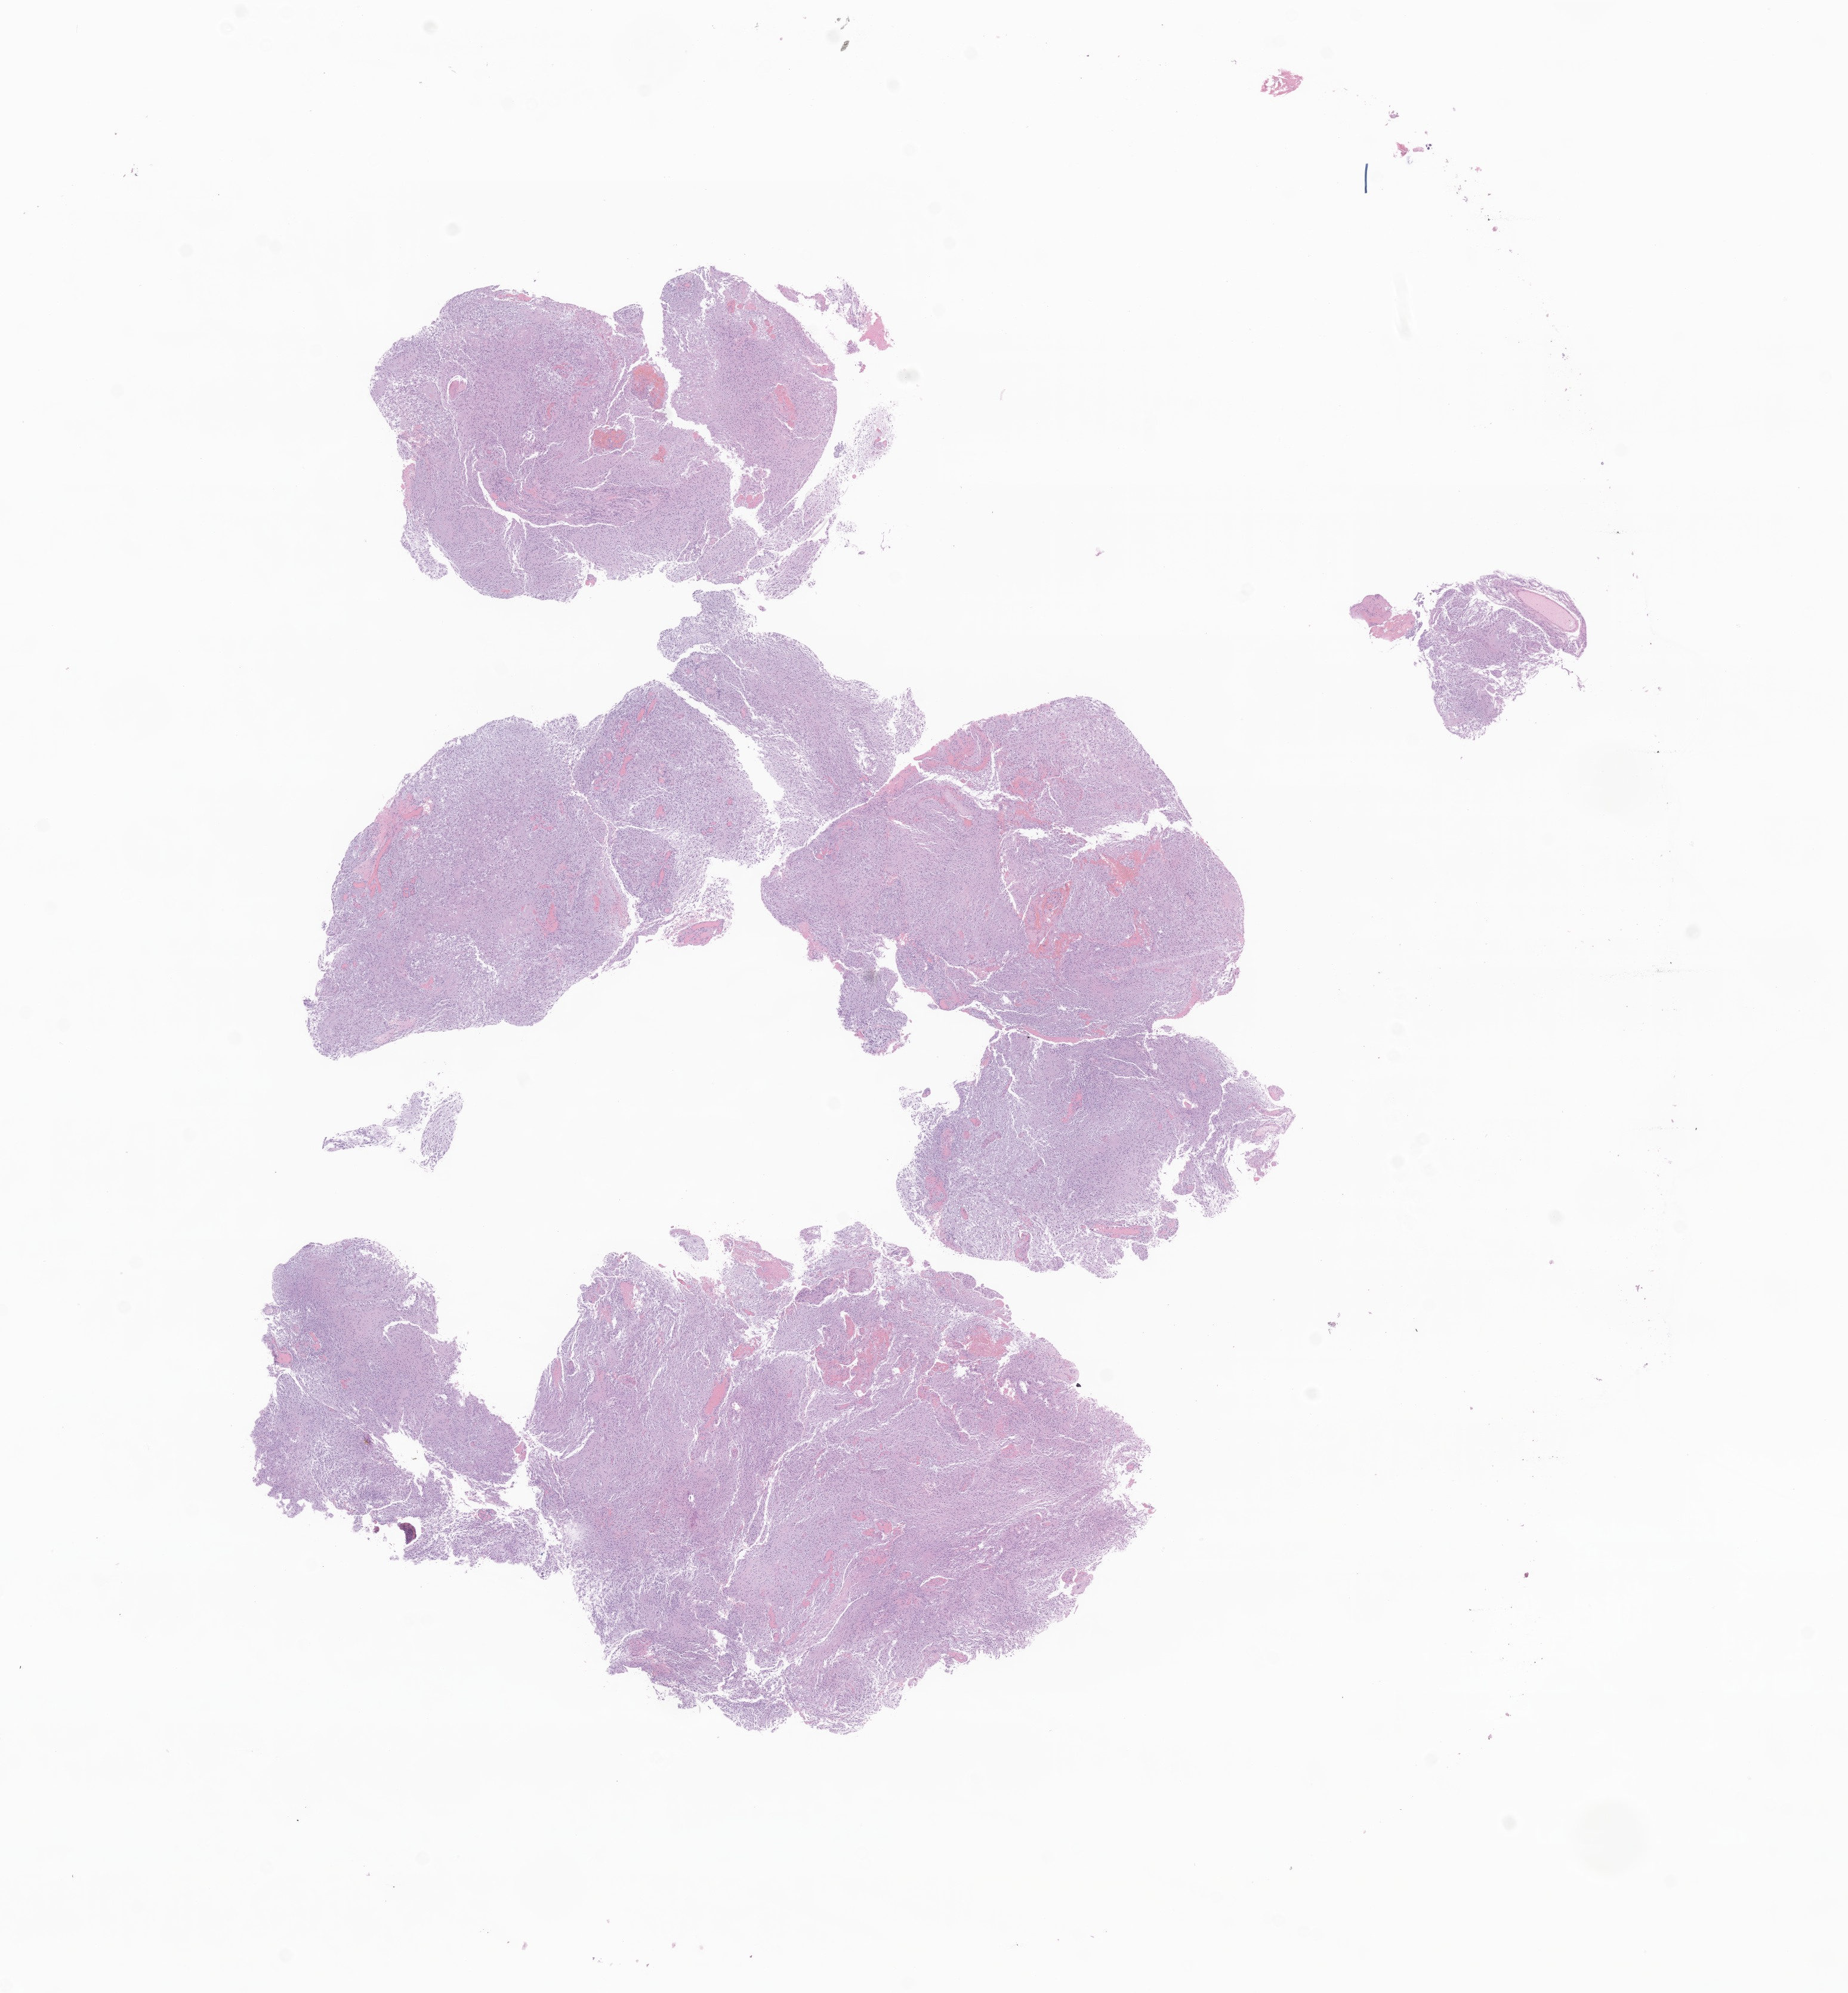
Haematoxylin and eosin whole-slide image of tumor tissue from the cerebral ventricle — shown as a low-resolution overview of the whole scanned area (about 13.1 x 14.1 mm). Formalin-fixed, paraffin-embedded (FFPE) tissue. Male patient, age 161 months.
Diagnosis: Pilocytic astrocytoma.